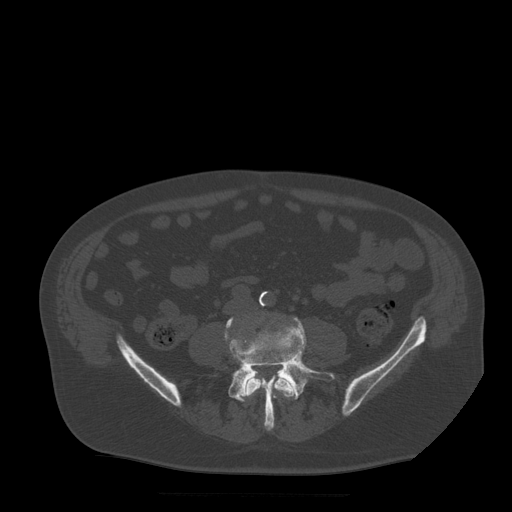
CT including the spine, one axial slice; slice 98 of 522 in the series (ordered by position); bone window (W 1800 / L 400 HU); 1.25 mm slice thickness; 512 × 512 image matrix, field of view 420 × 420 mm. Patient age 72 years. Case-level facts recorded for this patient, not image findings: primary cancer: prostate.
Annotated regions visible in this slice (semi-automatically segmented with operator editing):
- L4 vertebra: bounding box <244,370,298,399> (left, top, right, bottom; pixels)
- L5 vertebra: <225,317,336,430>